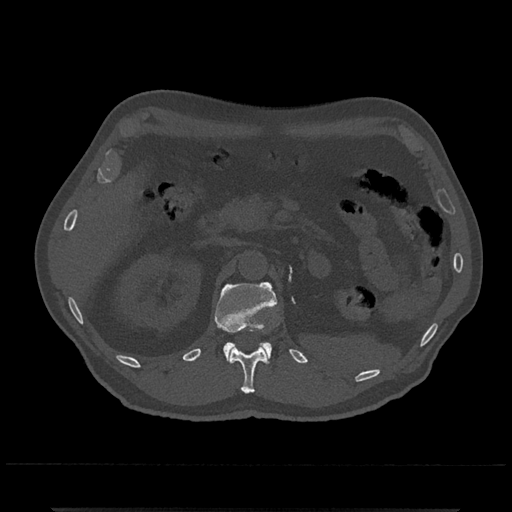
CT including the spine, one axial slice. Slice 398 of 797 in the series (ordered by position). 120 kVp. Bone window (W 1800 / L 400 HU). 0.5 mm slice thickness. 512 × 512 image matrix, field of view 393 × 393 mm. Patient: male, 67 years. Case-level facts recorded for this patient, not image findings: primary cancer: prostate.
Annotated regions visible in this slice (semi-automatic segmentation, software-assisted and operator-edited):
- L1 vertebra: bounding box (x1, y1, x2, y2) in pixels: (214, 282, 278, 363)
- T12 vertebra: (230, 329, 268, 394)